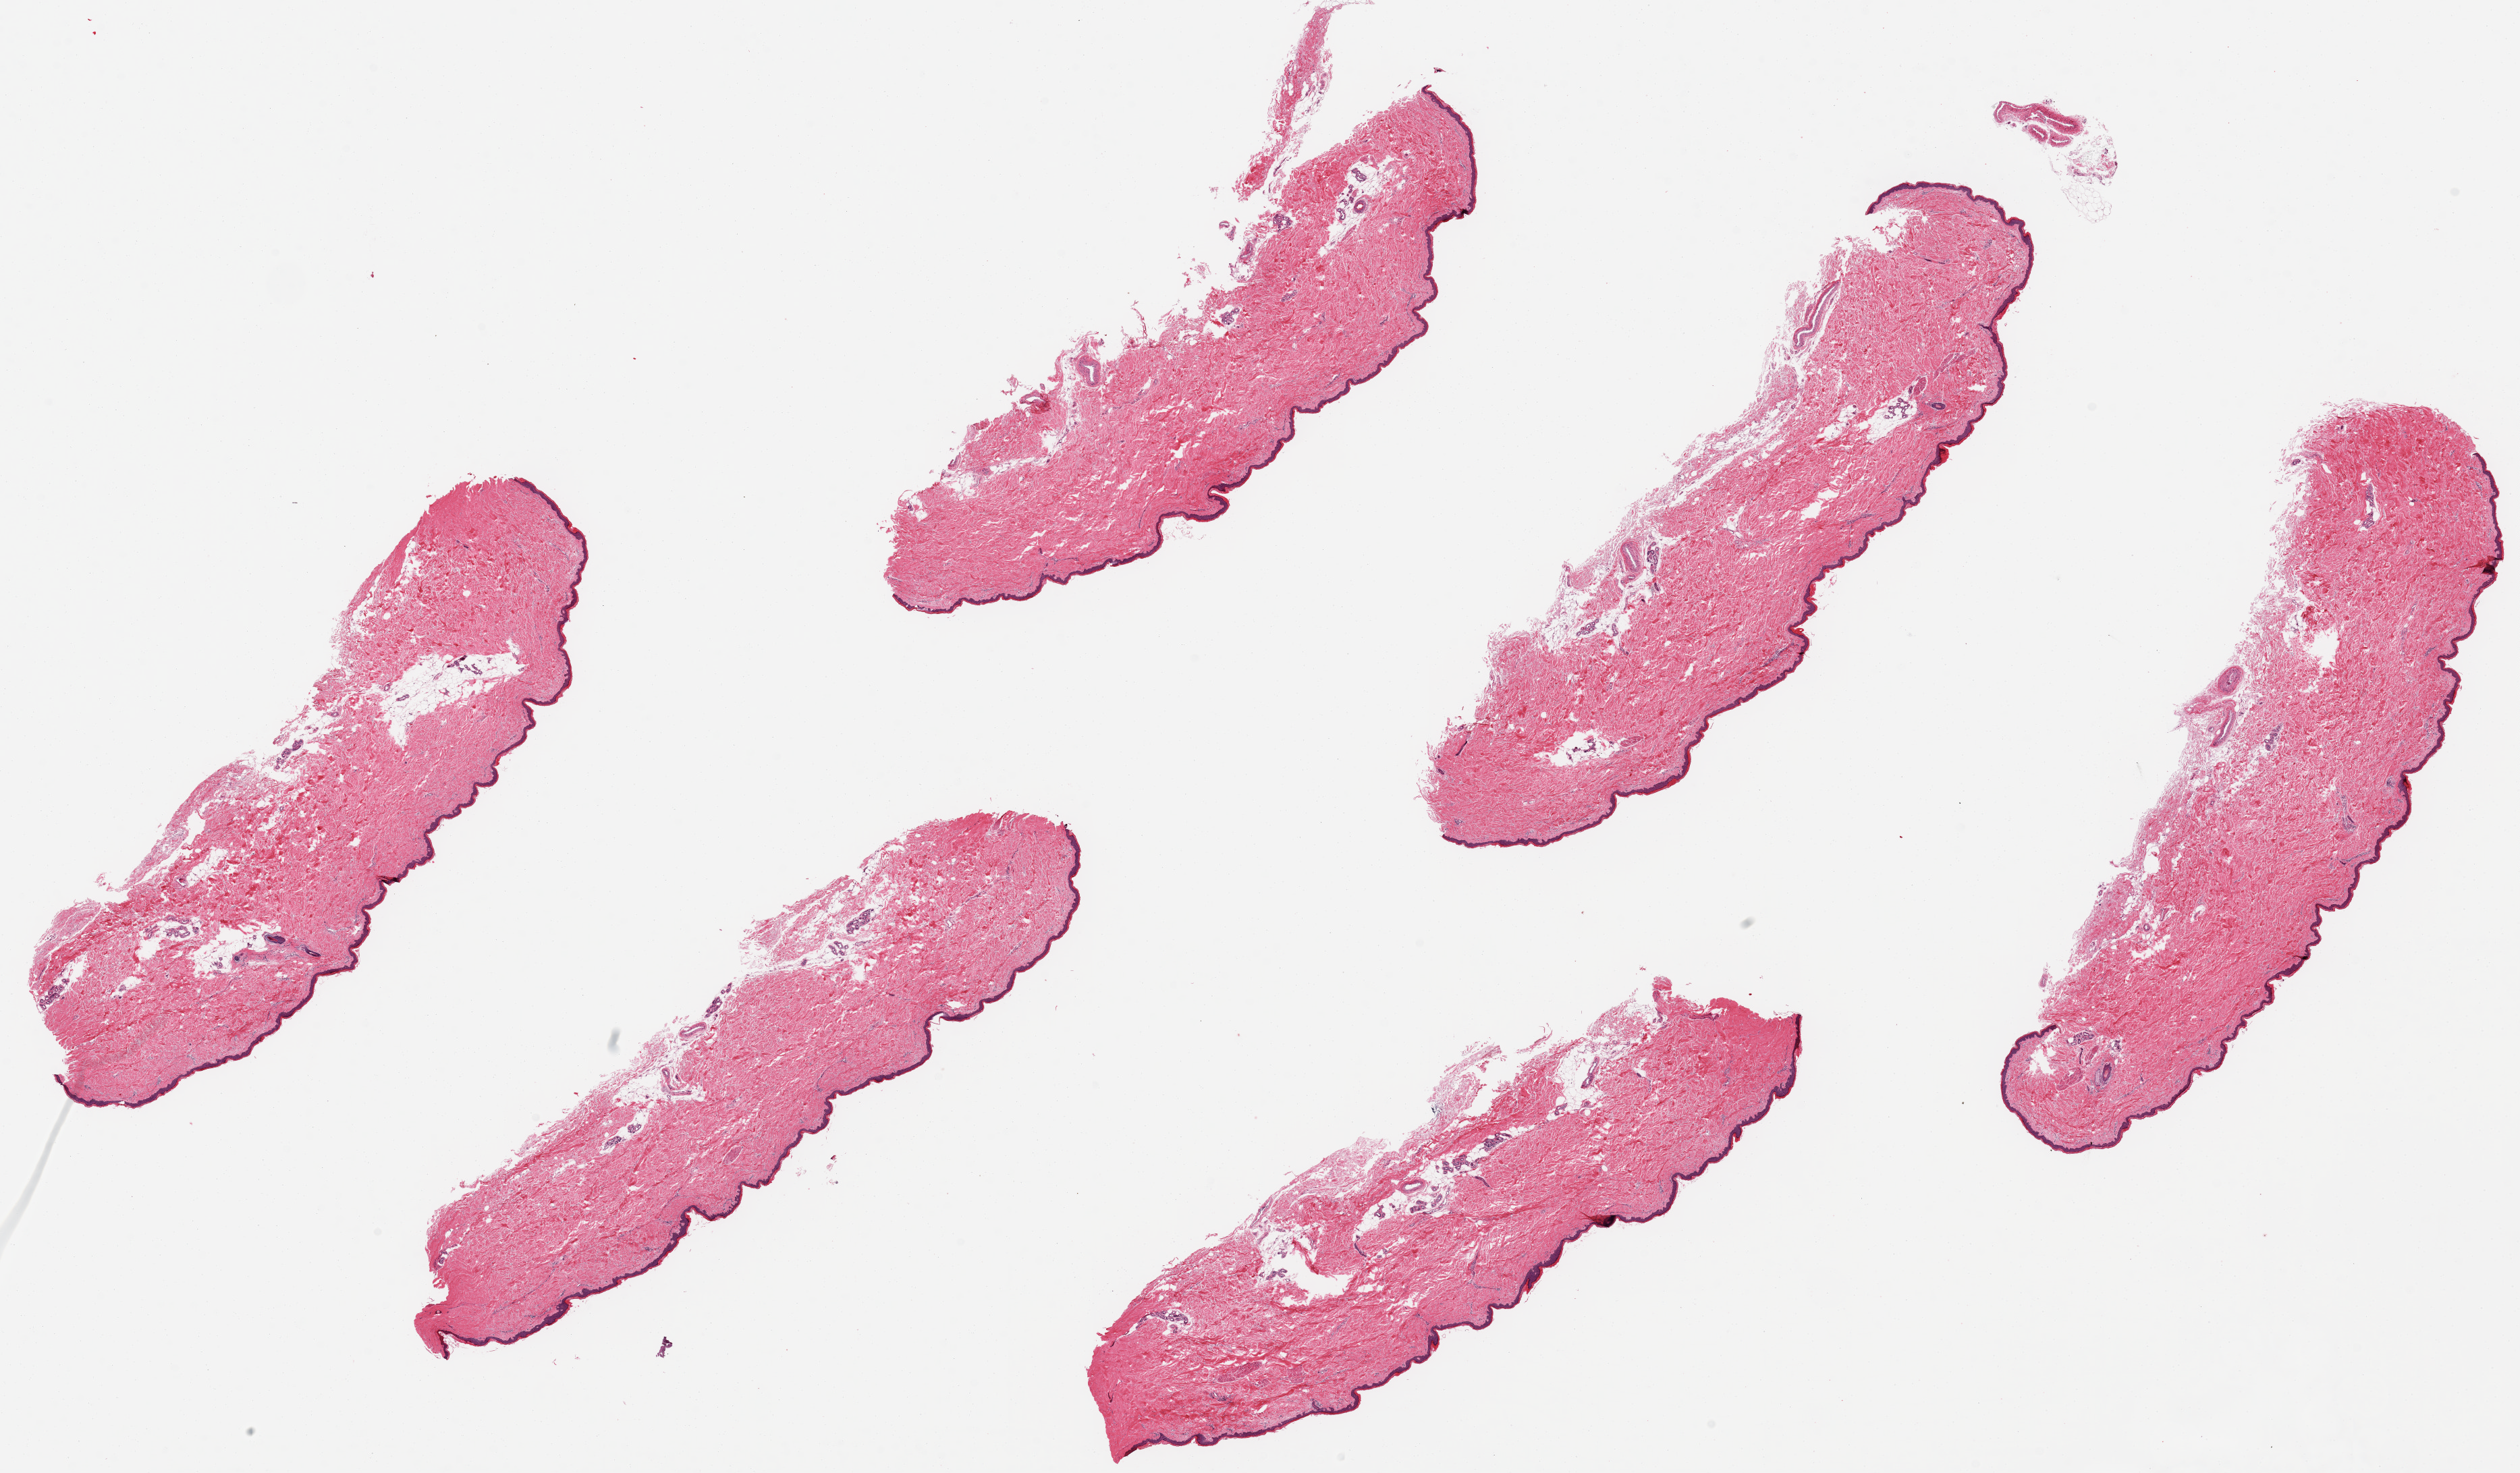
Digitized H&E-stained section — whole scanned area (about 29.5 x 17.3 mm) shown as a low-resolution overview, PAXgene-fixed, paraffin-embedded tissue, sampled site (target tissue): skin of lower leg, donor tissue sample. Female donor.
Pathologist's review note for this sample: 6 pieces, ~9x2mm, squamous epithelium is ~ 2% of thickness.